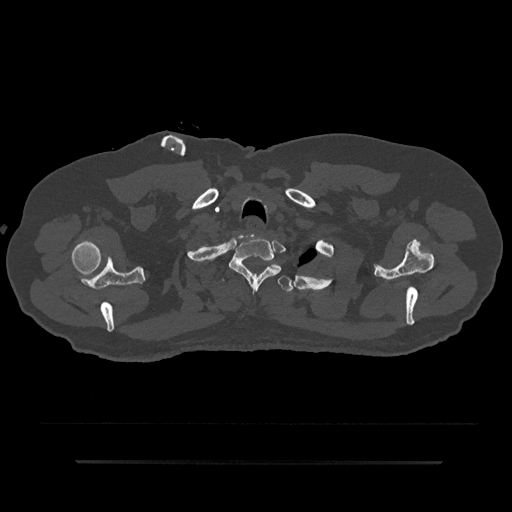
CT including the spine, one axial slice. Position 729 of 797 along the scan axis. Reconstruction kernel Br40s/3. Bone window (W 1800 / L 400 HU). 0.5 mm slice thickness. 512 × 512 image matrix, field of view 464 × 464 mm. Male patient, age 59 years. Case-level facts recorded for this patient, not image findings: primary cancer: bile ducts.
Annotated regions visible in this slice (semi-automatic segmentation, software-assisted and operator-edited):
- T1 vertebra: bounding box [x1, y1, x2, y2] px = [229, 235, 281, 291]
- T2 vertebra: [219, 264, 293, 292]